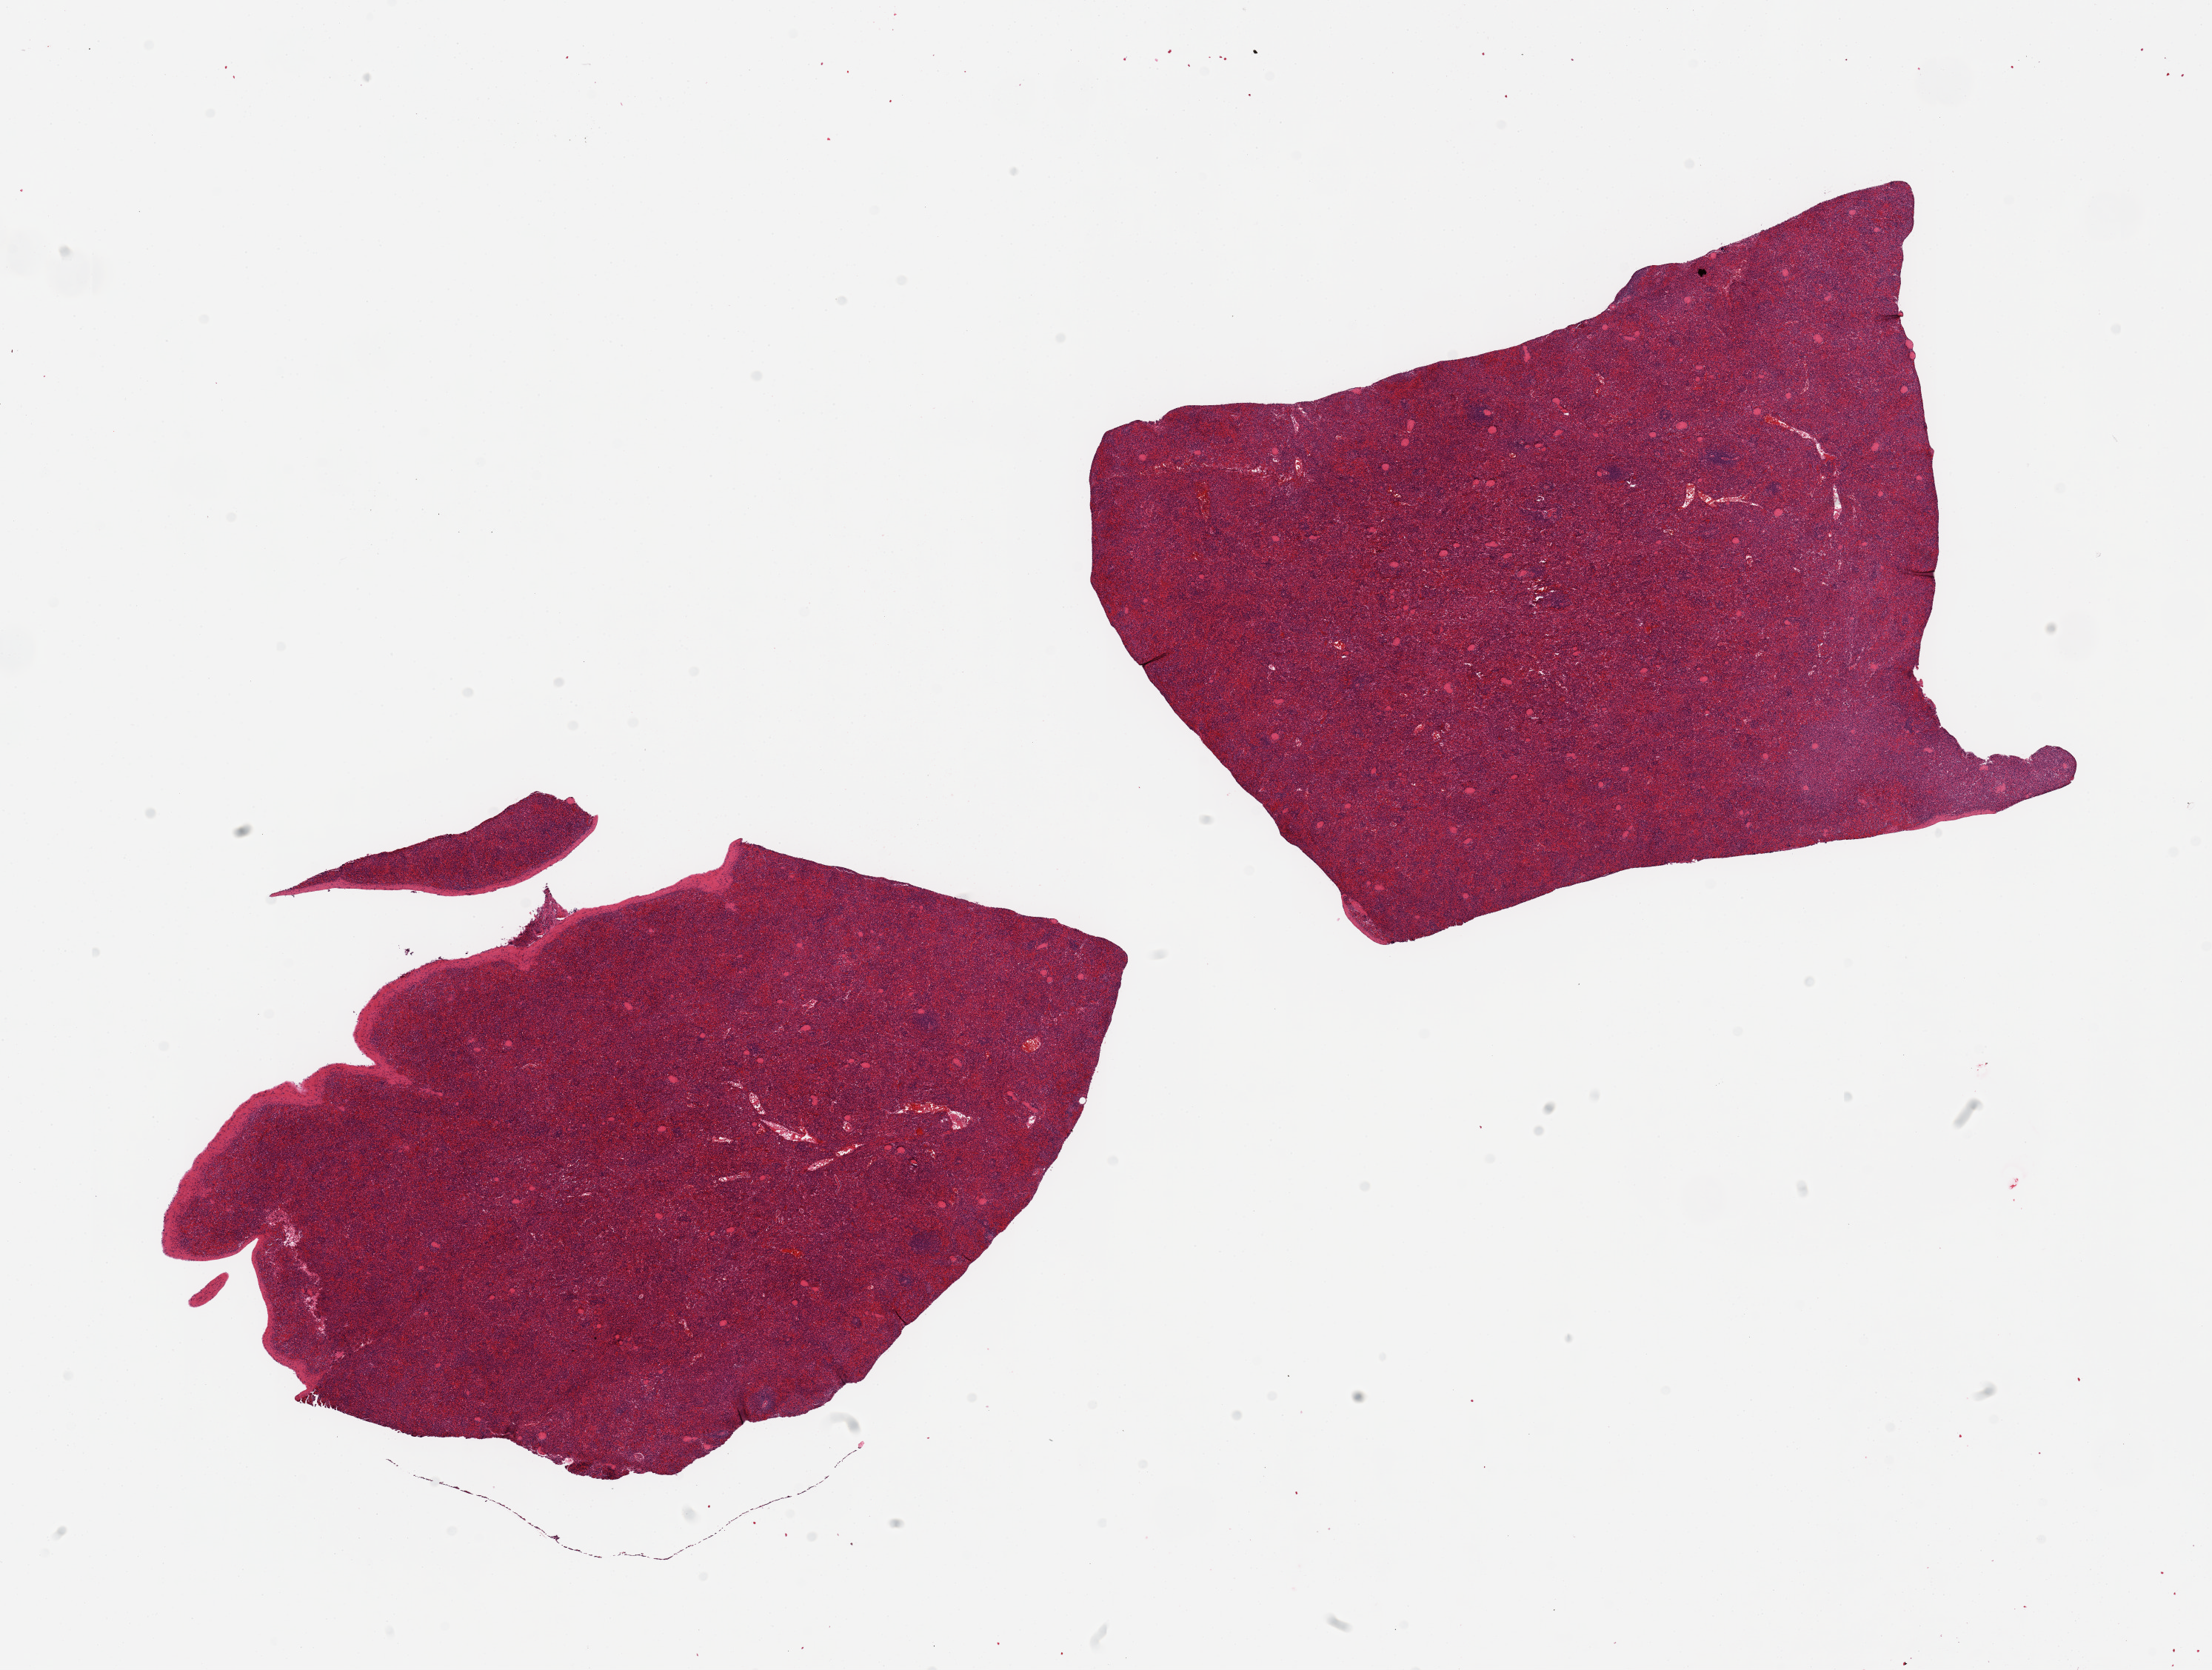
Whole-slide image, H&E stain, brightfield — low-resolution overview of the scanned area, about 23.6 x 17.8 mm (from a 20x scan); PAXgene-fixed paraffin-embedded (PFPE) section; section of spleen (target tissue); tissue donor sample.
Review note (as recorded): 2 pieces; capsule is present (target is 5mm below capsule), congestion, diminished white pulp.